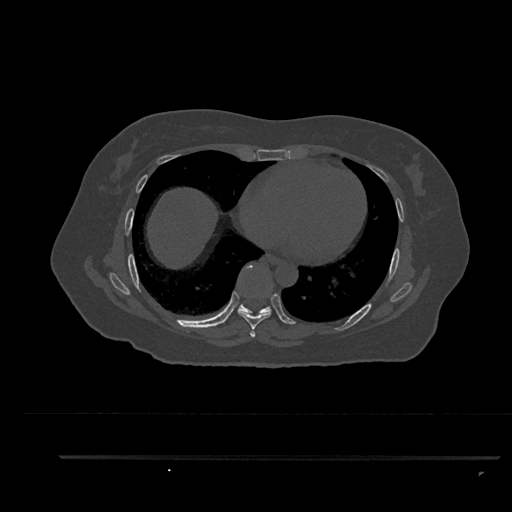
CT including the spine, one axial slice; slice 490 of 797 in the series (ordered by position); reconstruction kernel Br40s/3; 120 kVp; bone window (W 1800 / L 400 HU); 0.5 mm slice thickness; 512 × 512 image matrix, field of view 408 × 408 mm. Patient: female, 44 years. Case-level facts recorded for this patient, not image findings: primary cancer: renal; vertebrae with lytic lesions (as recorded): L1.
Structures marked on this image (semi-automatic segmentation, software-assisted and operator-edited):
- T6 vertebra: box from (x=251, y=334) to (x=255, y=337) px
- T7 vertebra: (x=238, y=265)–(x=271, y=338)
- T8 vertebra: (x=237, y=265)–(x=271, y=316)